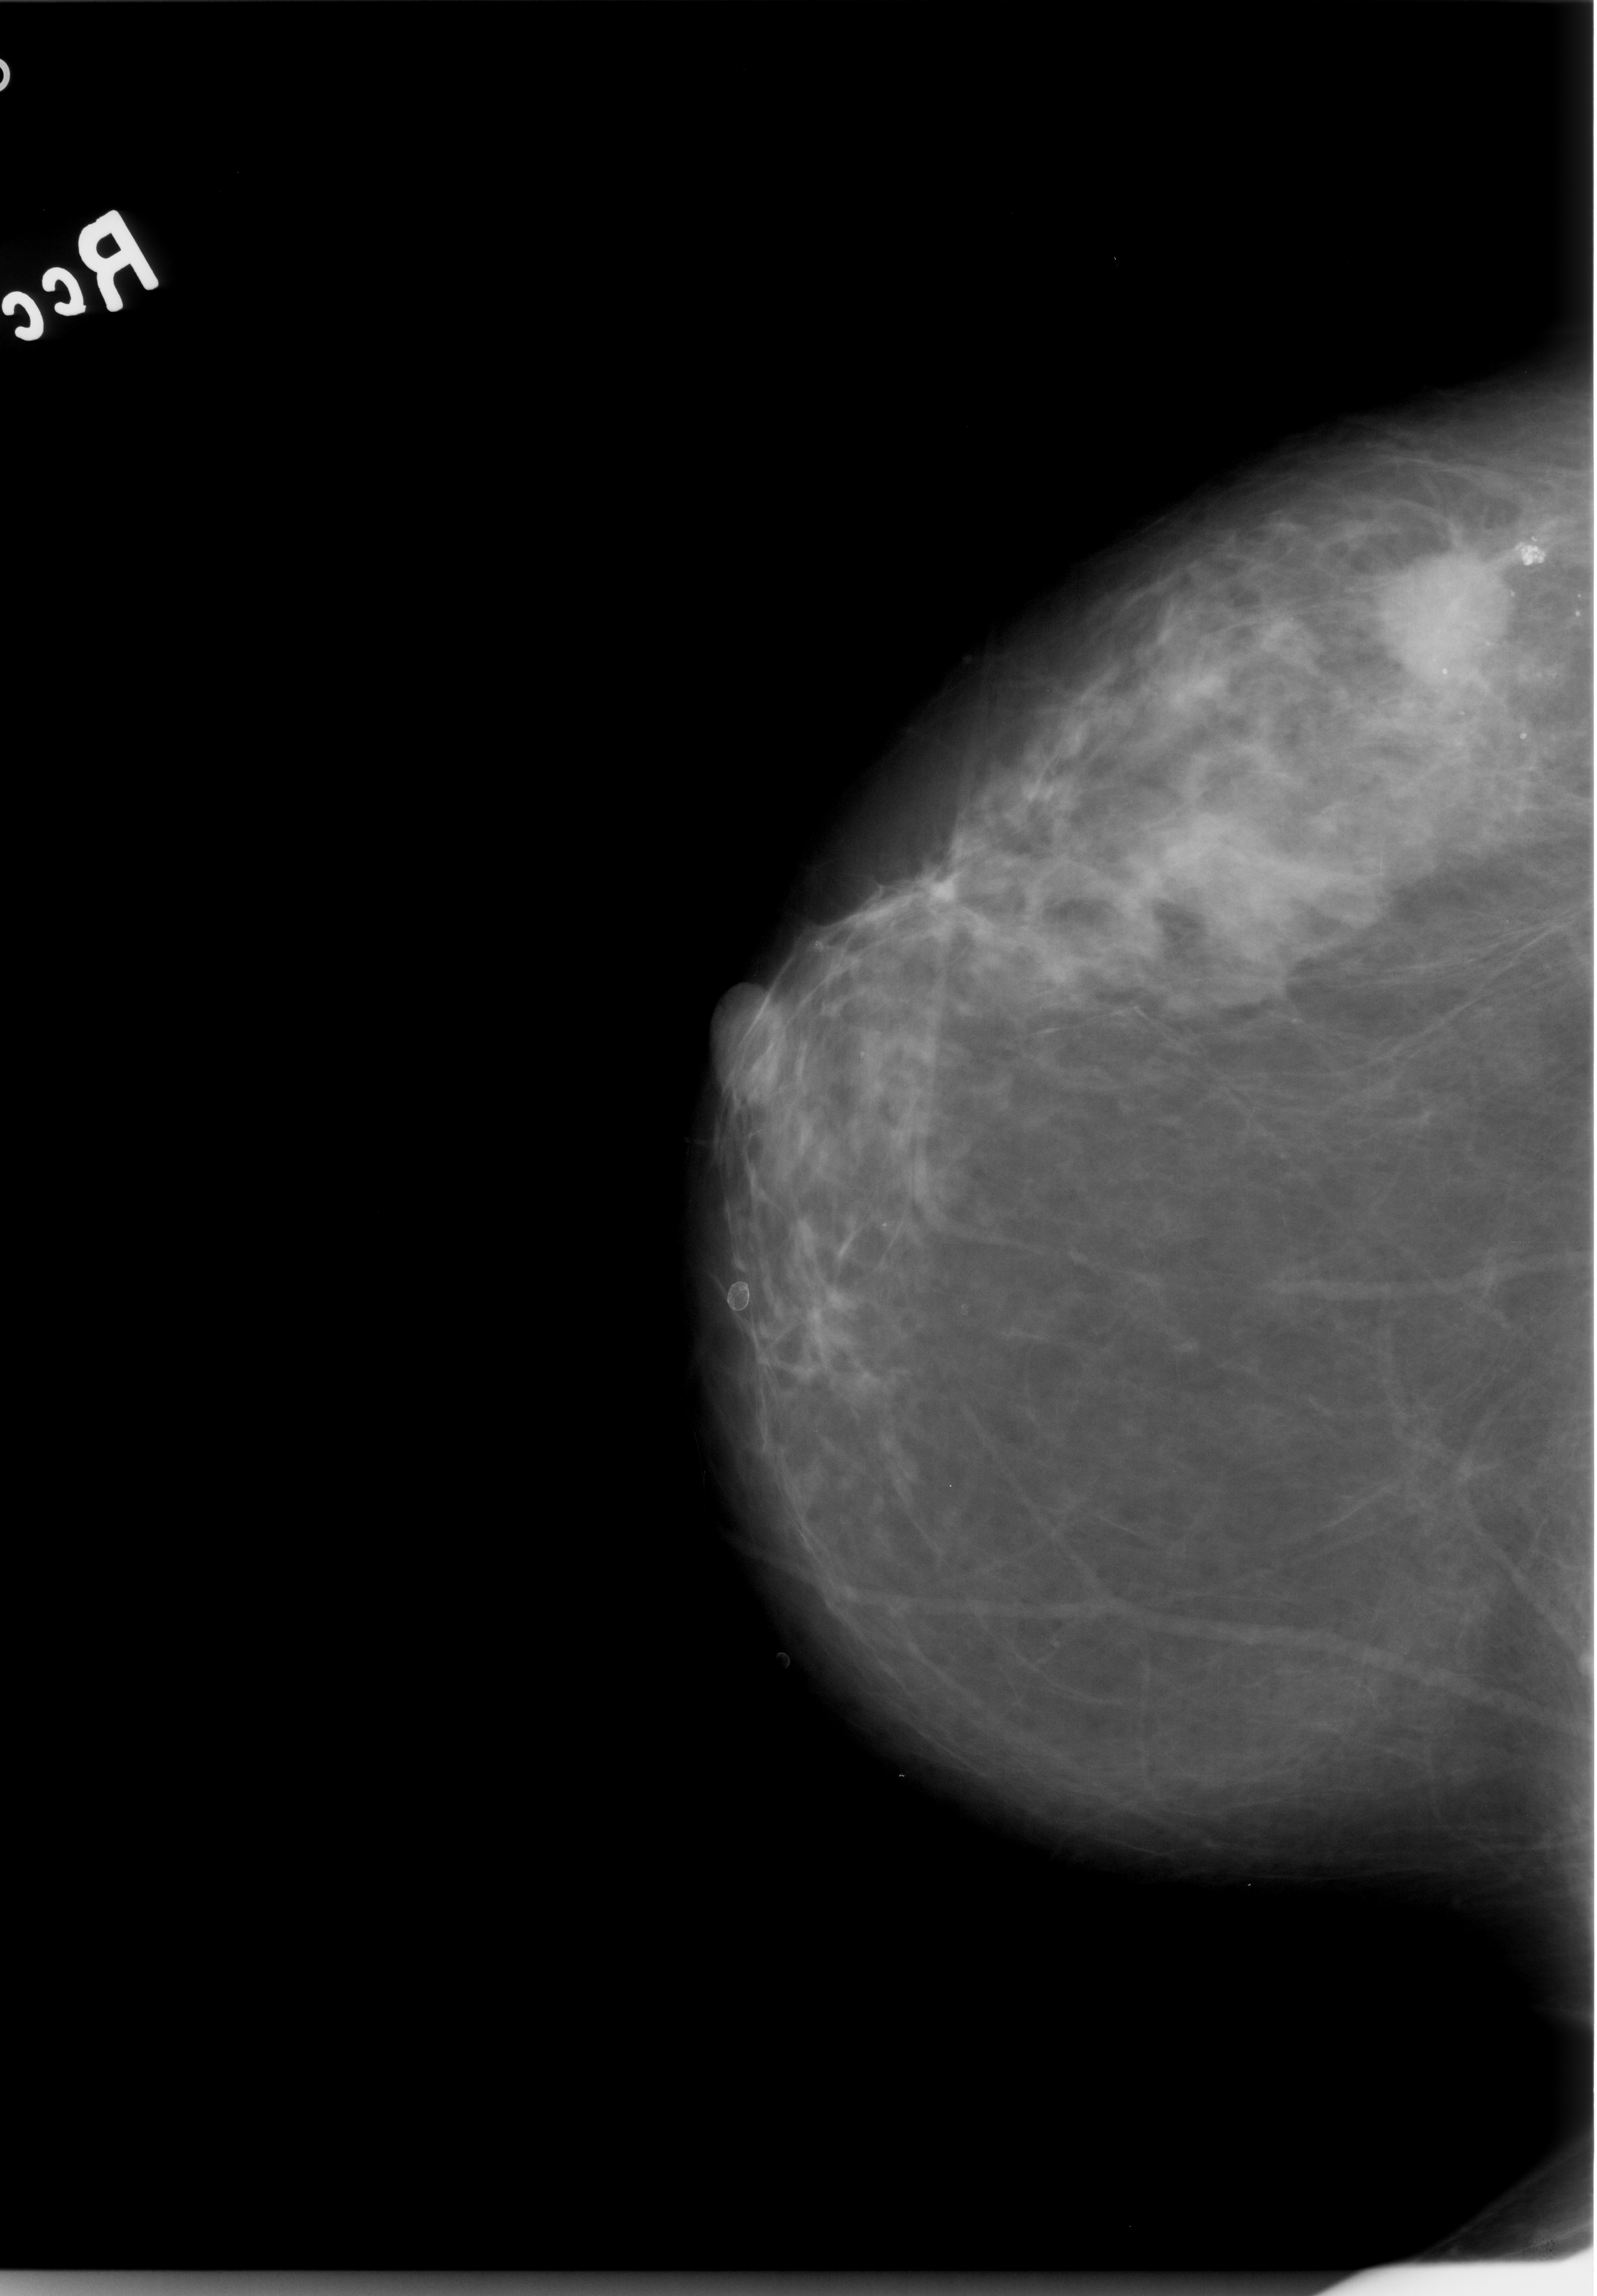
Digitized screen-film mammogram; right breast; CC view; breast composition: scattered fibroglandular densities (BI-RADS density category 2 of 4); 1597 × 2296 image matrix.
Marked abnormalities (boxes around the expert regions of interest):
- mass, shape irregular, margins spiculated; BI-RADS assessment category 4; pathology (as recorded): malignant: bounding box (x1, y1, x2, y2) in pixels: (1355, 529, 1519, 684)